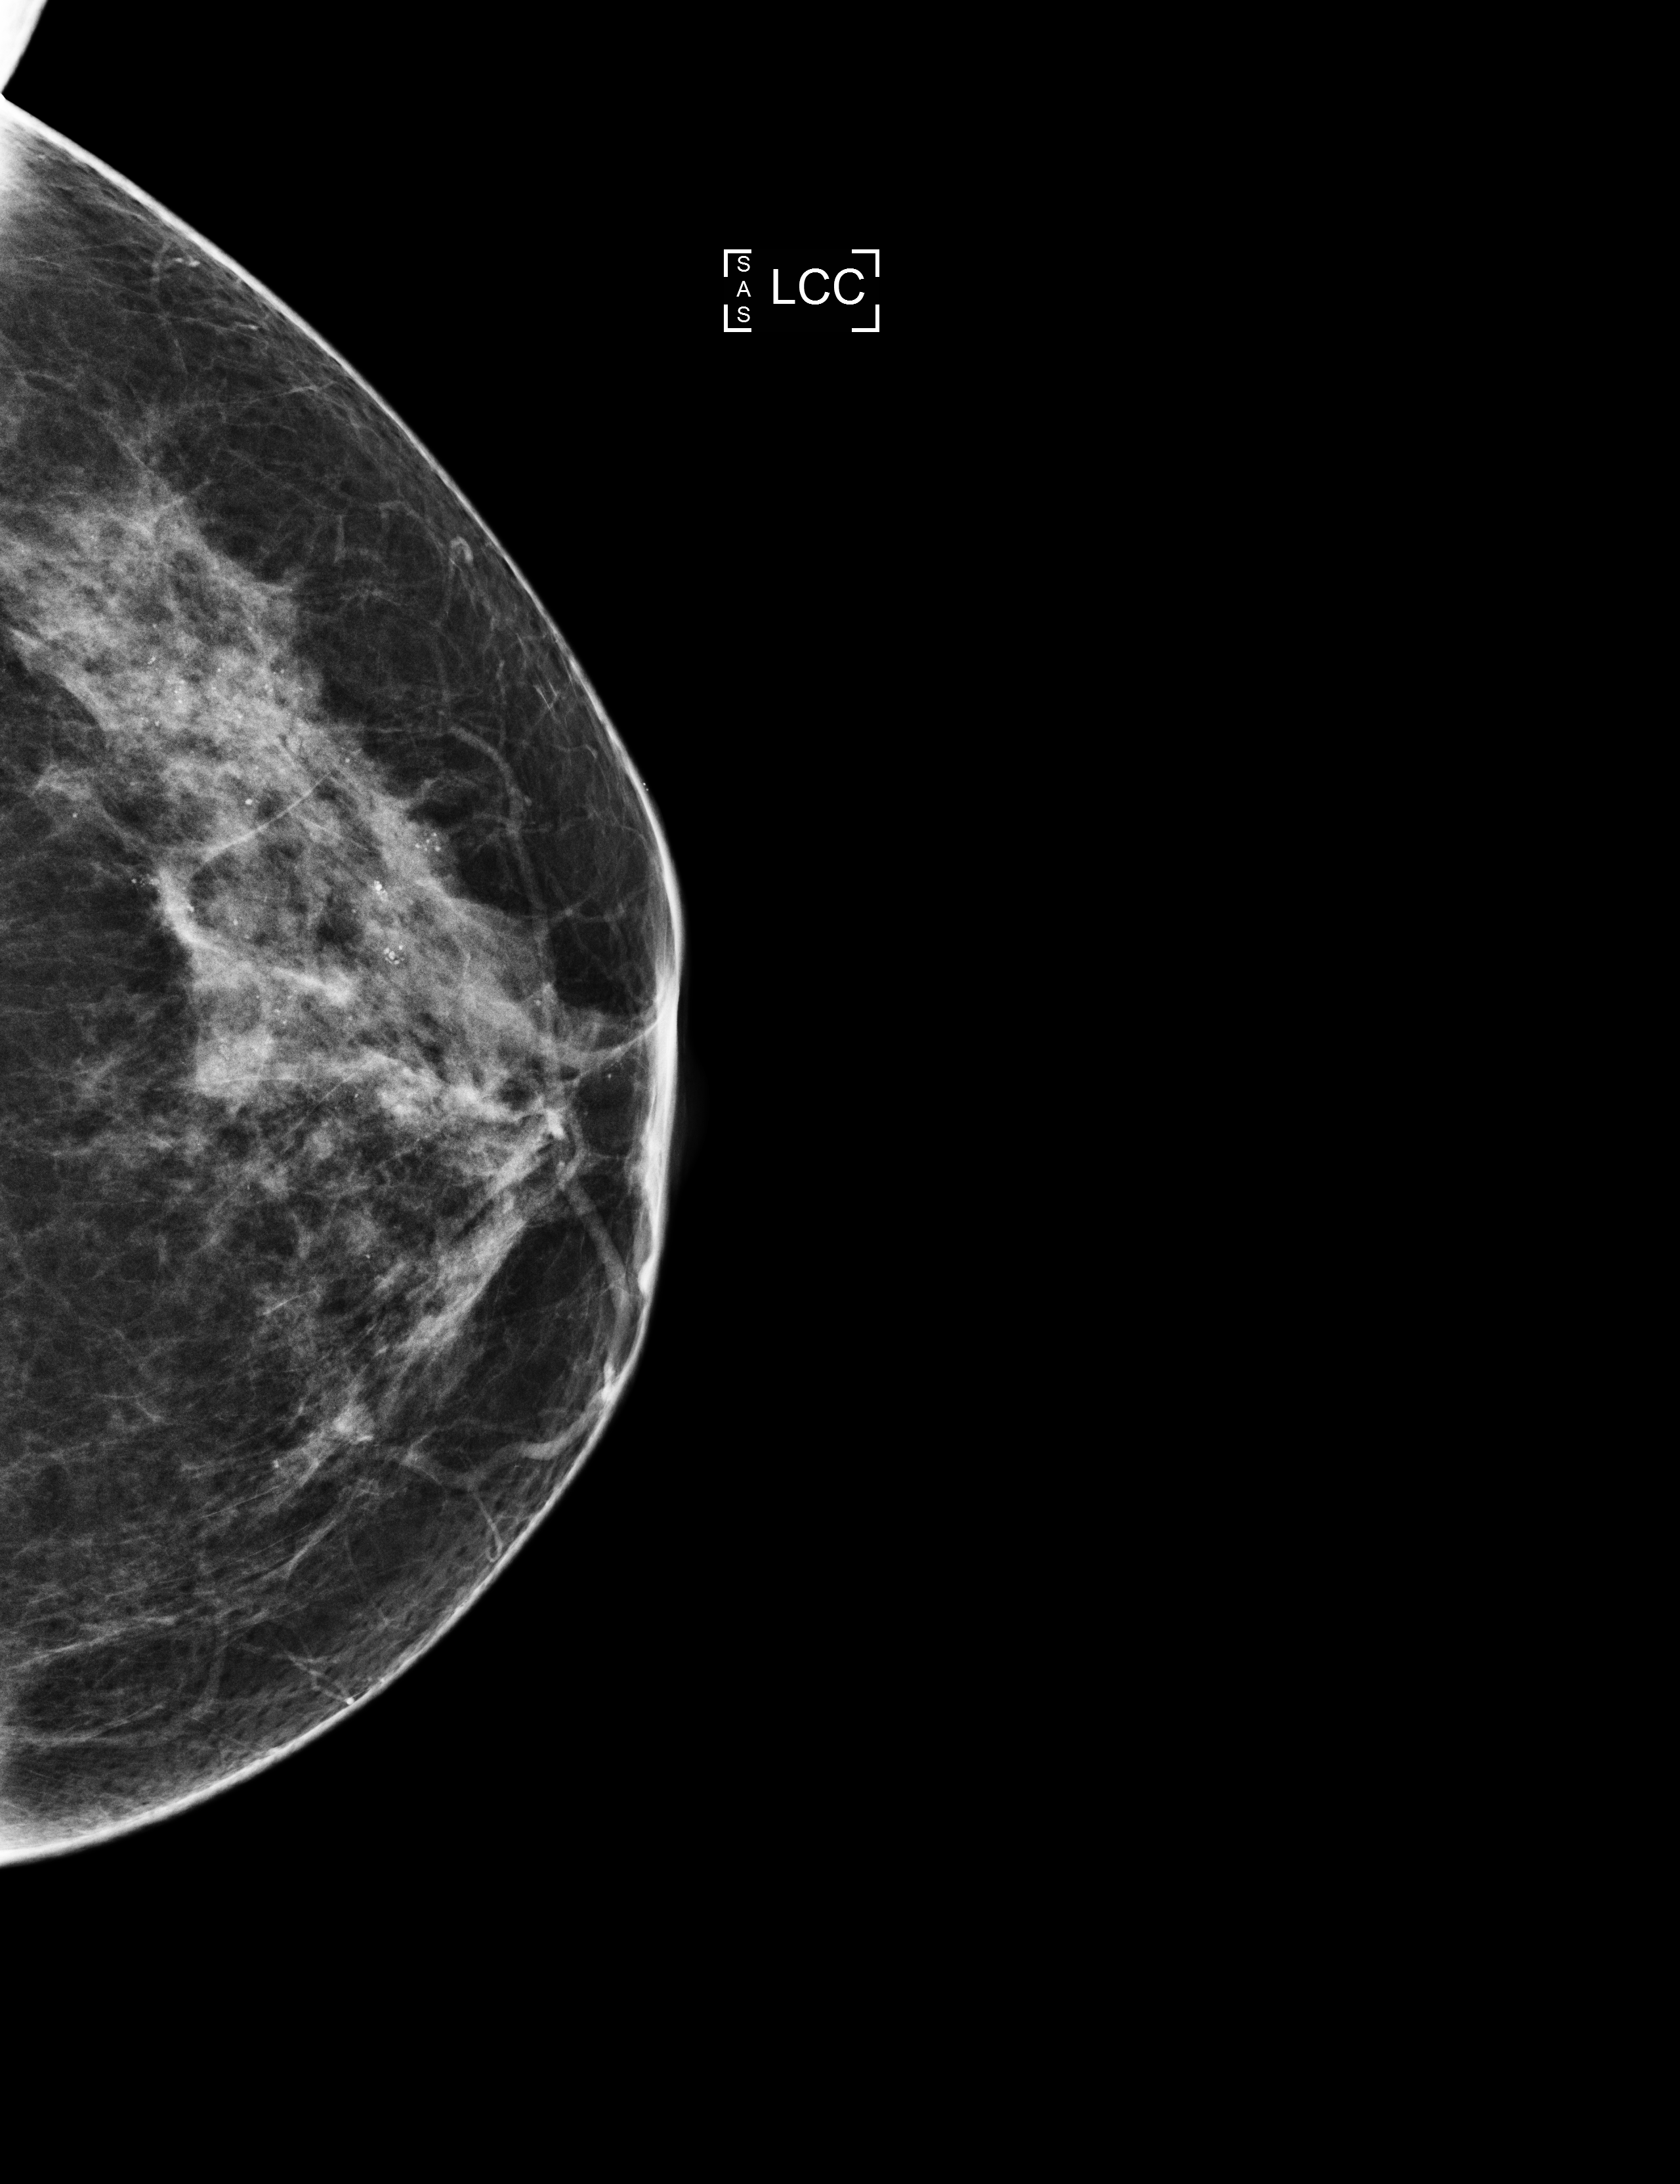
Annual screening mammography examination; compressed breast thickness 52 mm; system: Selenia Dimensions. Patient aged 51 years (female).
Image type: full-field digital mammogram. Breast: left. Projection: CC view.